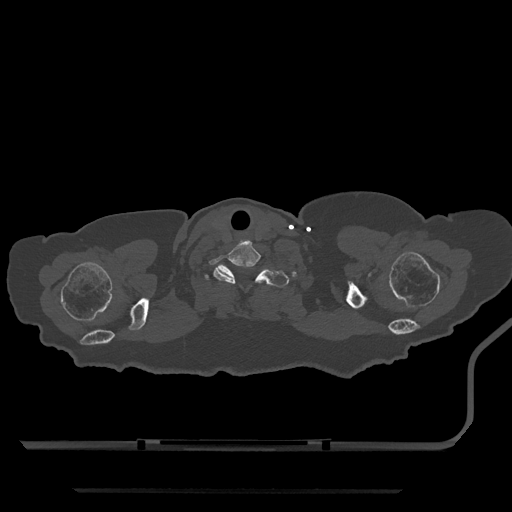
CT including the spine, one axial slice; position 726 of 797 along the scan axis; reconstruction kernel Br40s/3; 120 kVp; bone window (W 1800 / L 400 HU); 0.5 mm slice thickness; 512 × 512 image matrix, field of view 440 × 440 mm. Patient: female, 51 years. From the clinical record (not read from this slice): primary cancer: neuro; vertebrae with lytic lesions (as recorded): T8.
Structures marked on this image (semi-automatically segmented with operator editing):
- T1 vertebra: bounding box (x1, y1, x2, y2) in pixels: (205, 264, 289, 287)